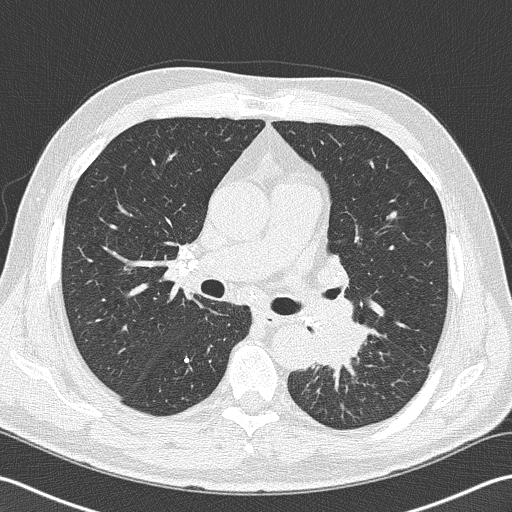
Low-dose screening chest CT, axial slice; second screening round (one year after baseline); lung window (W 1500 / L -600 HU); 2 mm slice thickness; 512 × 512 image matrix. Male participant, aged 57 years at enrolment. Former smoker at enrolment.
Expert-annotated lung lesion, box from (x=294, y=307) to (x=374, y=384) px. The exam's reader record, not a measurement of the box and not confirmed to be the same lesion: non-calcified nodule or mass ≥4 mm, left lower lobe, 40 × 30 mm, spiculated (stellate) margins, soft tissue attenuation, pre-existing on the prior screen: no. Lung cancer was diagnosed 9 days after this screen: squamous cell carcinoma, NOS, left lower lobe, moderately differentiated (G2), stage IIIB (AJCC 6th edition), 38 mm at pathology.